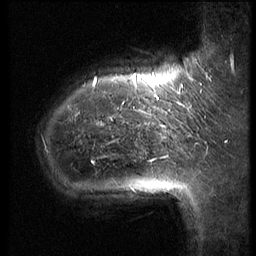
Breast MRI (dynamic contrast-enhanced), one sagittal slice; slice 10 of 62 in the series (ordered by position); 3 images stored at this slice position (order not interpretable as contrast timing); 1.5 T; TE 4.2 ms, TR 9 ms; 2.5 mm slice thickness; 256 × 256 image matrix, field of view 180 × 180 mm. Female patient, age 39 years. From the clinical record (not read from this slice): setting: breast cancer imaged before/during neoadjuvant chemotherapy; receptor status: HER2-positive.
Annotated regions visible in this slice (semi-automatically segmented with operator editing):
- analysis volume of interest (the breast-tissue region the enhancement analysis was run in; not a lesion): bounding box (x1, y1, x2, y2) in pixels: (32, 64, 171, 221)
- tumour enhancement mask (voxels above the 140 % enhancement threshold inside the analysis volume of interest): (95, 74, 168, 163)